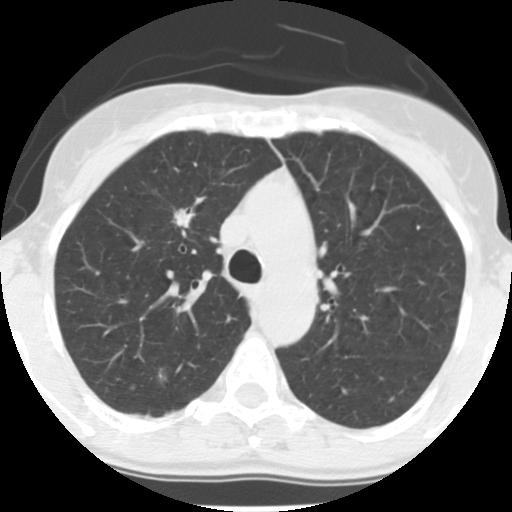
Low-dose screening chest CT, axial slice, second screening round (one year after baseline), lung window (W 1500 / L -600 HU), slice 46 of 150 in the series, 512 × 512 image matrix, field of view 280 × 280 mm. Female, age 56 years at enrolment.
Lesion marked by an expert reader, bounding box (x1, y1, x2, y2) in pixels: (161, 195, 205, 243). The exam's reader record, not a measurement of the box and not confirmed to be the same lesion: non-calcified nodule or mass ≥4 mm, right upper lobe, 12 × 9 mm, spiculated (stellate) margins, soft tissue attenuation, pre-existing on the prior screen: yes; interval growth: no. Lung cancer was diagnosed 350 days after this screen (after the third annual screen): adenocarcinoma, NOS, right upper lobe, moderately differentiated (G2), stage IA (AJCC 6th edition), 19 mm at pathology.